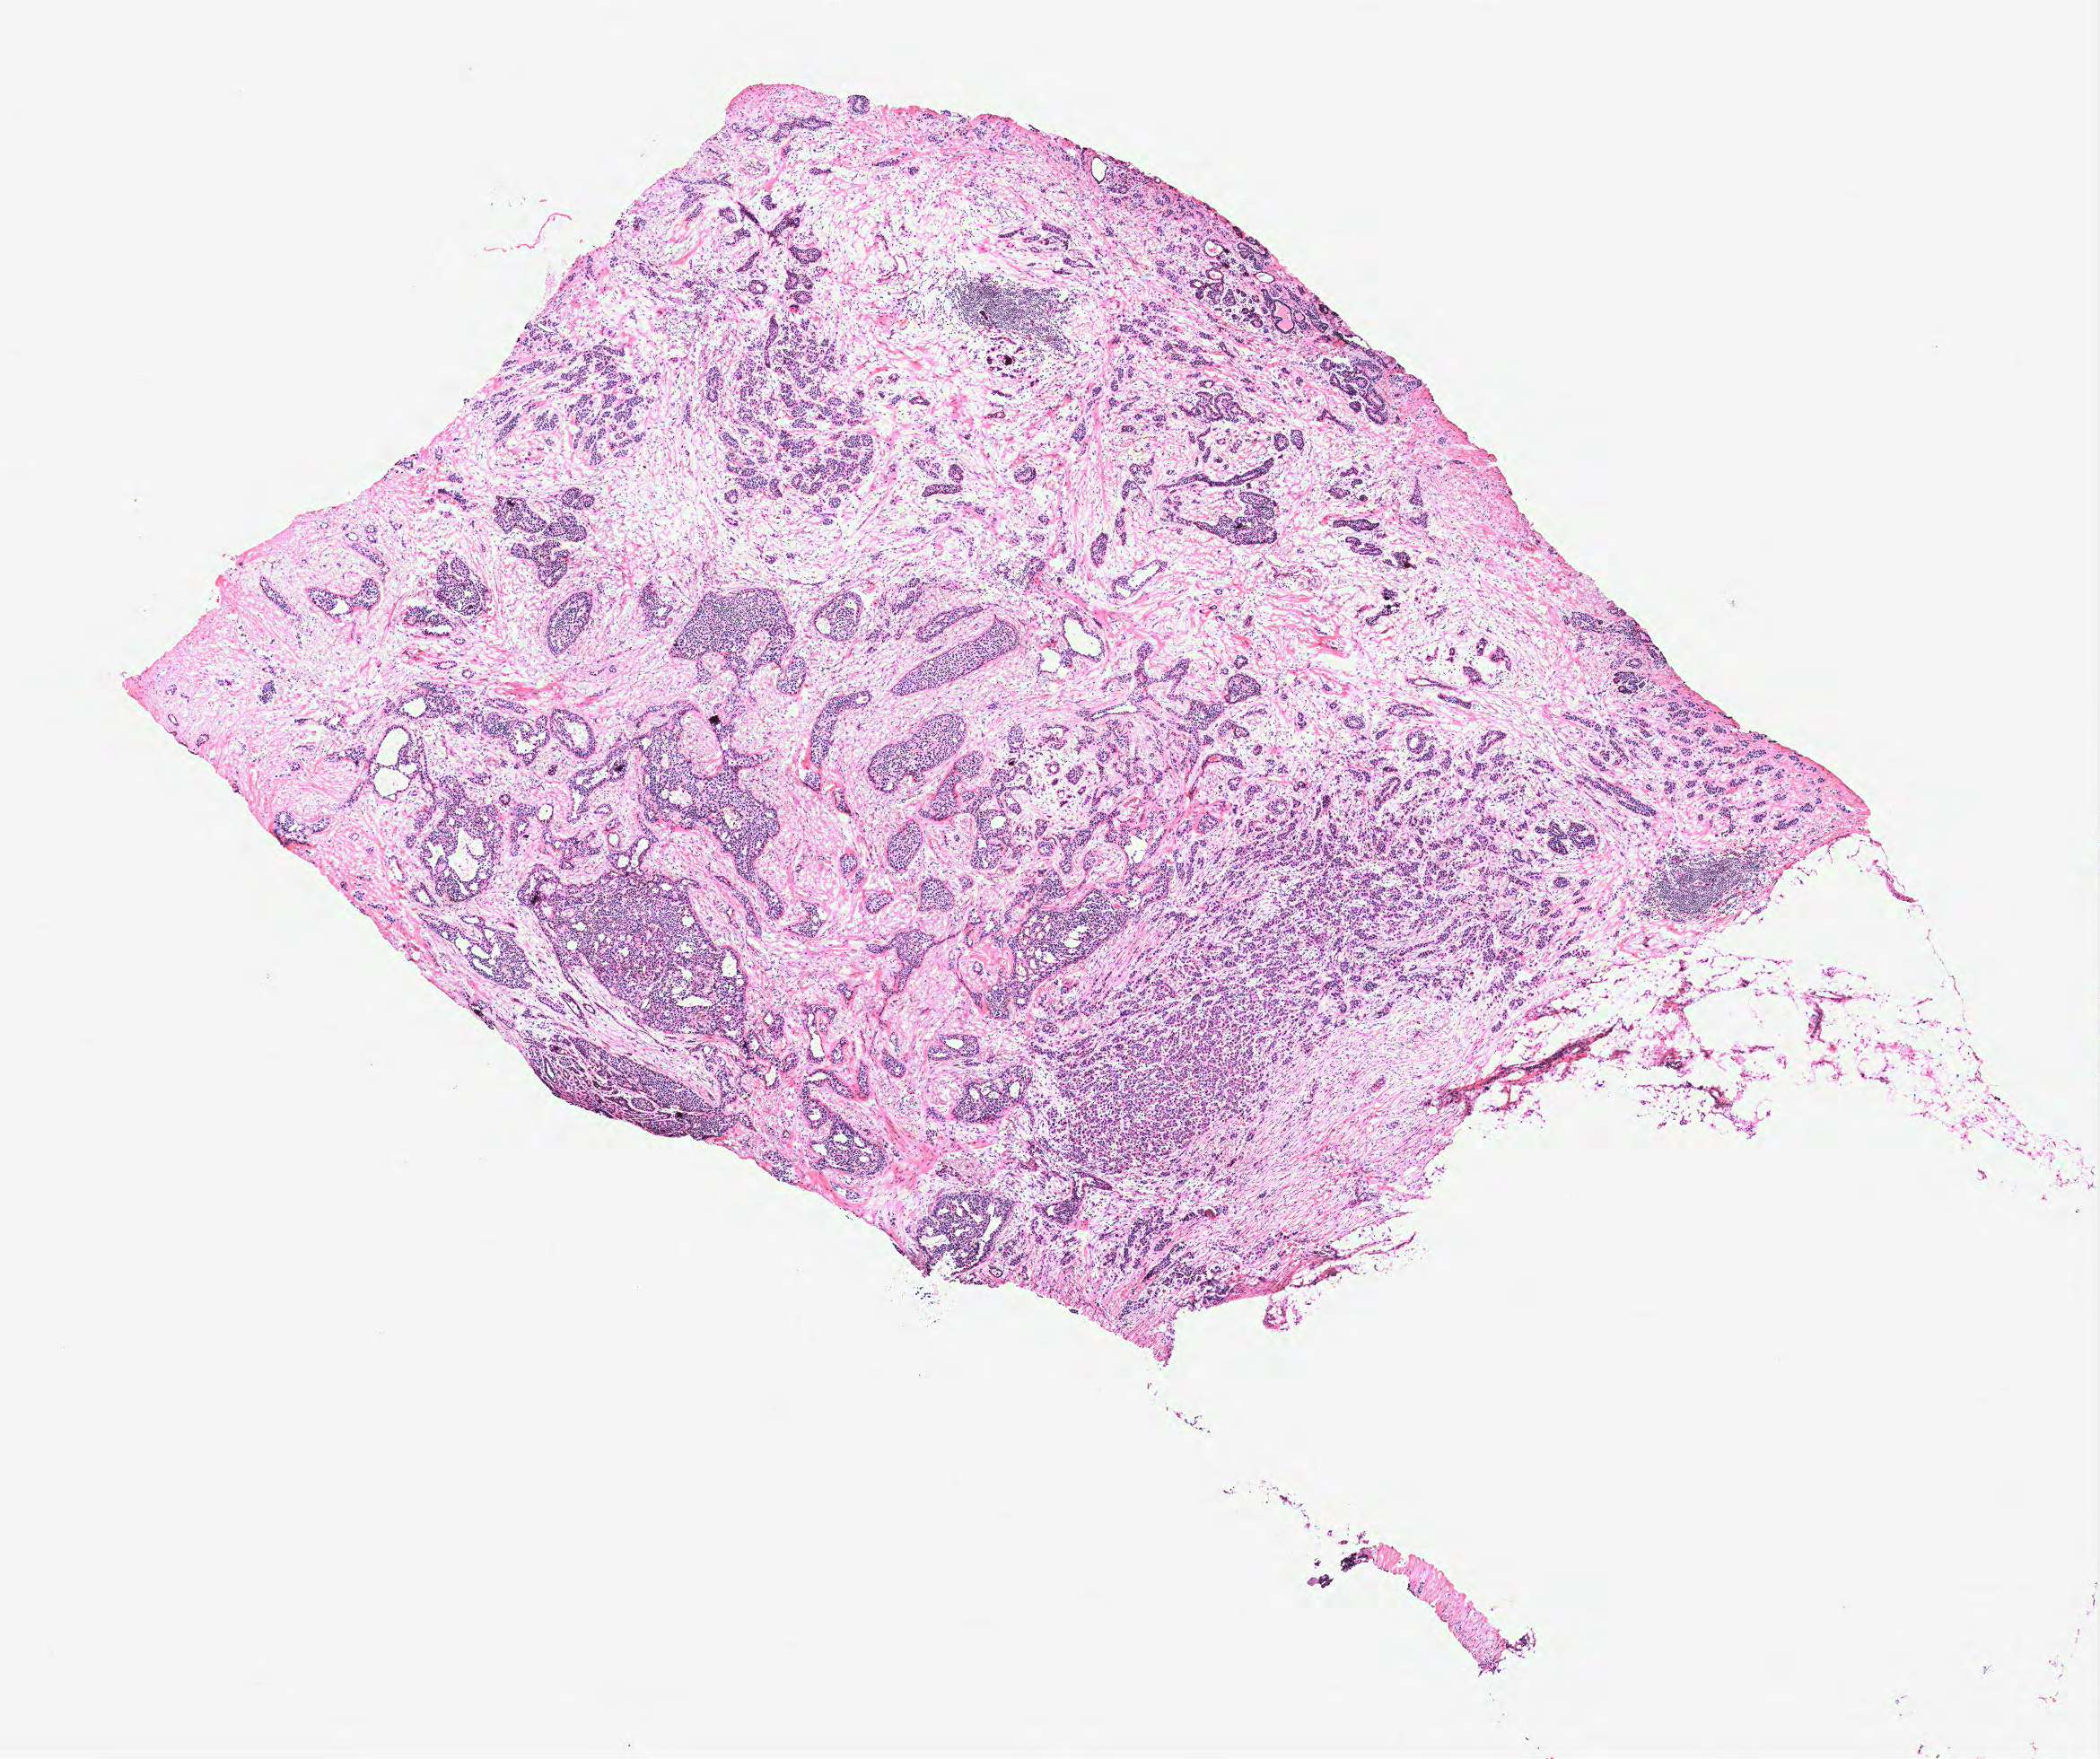
Digitized Hematoxylin and eosin (H&E) stained tissue section (whole slide), whole scanned area (about 9.4 x 7.8 mm, from a 40x scan) shown as a low-resolution overview, tumour tissue sample, breast. Patient: female, age 59 years.
Diagnosis: Infiltrating duct carcinoma, NOS.